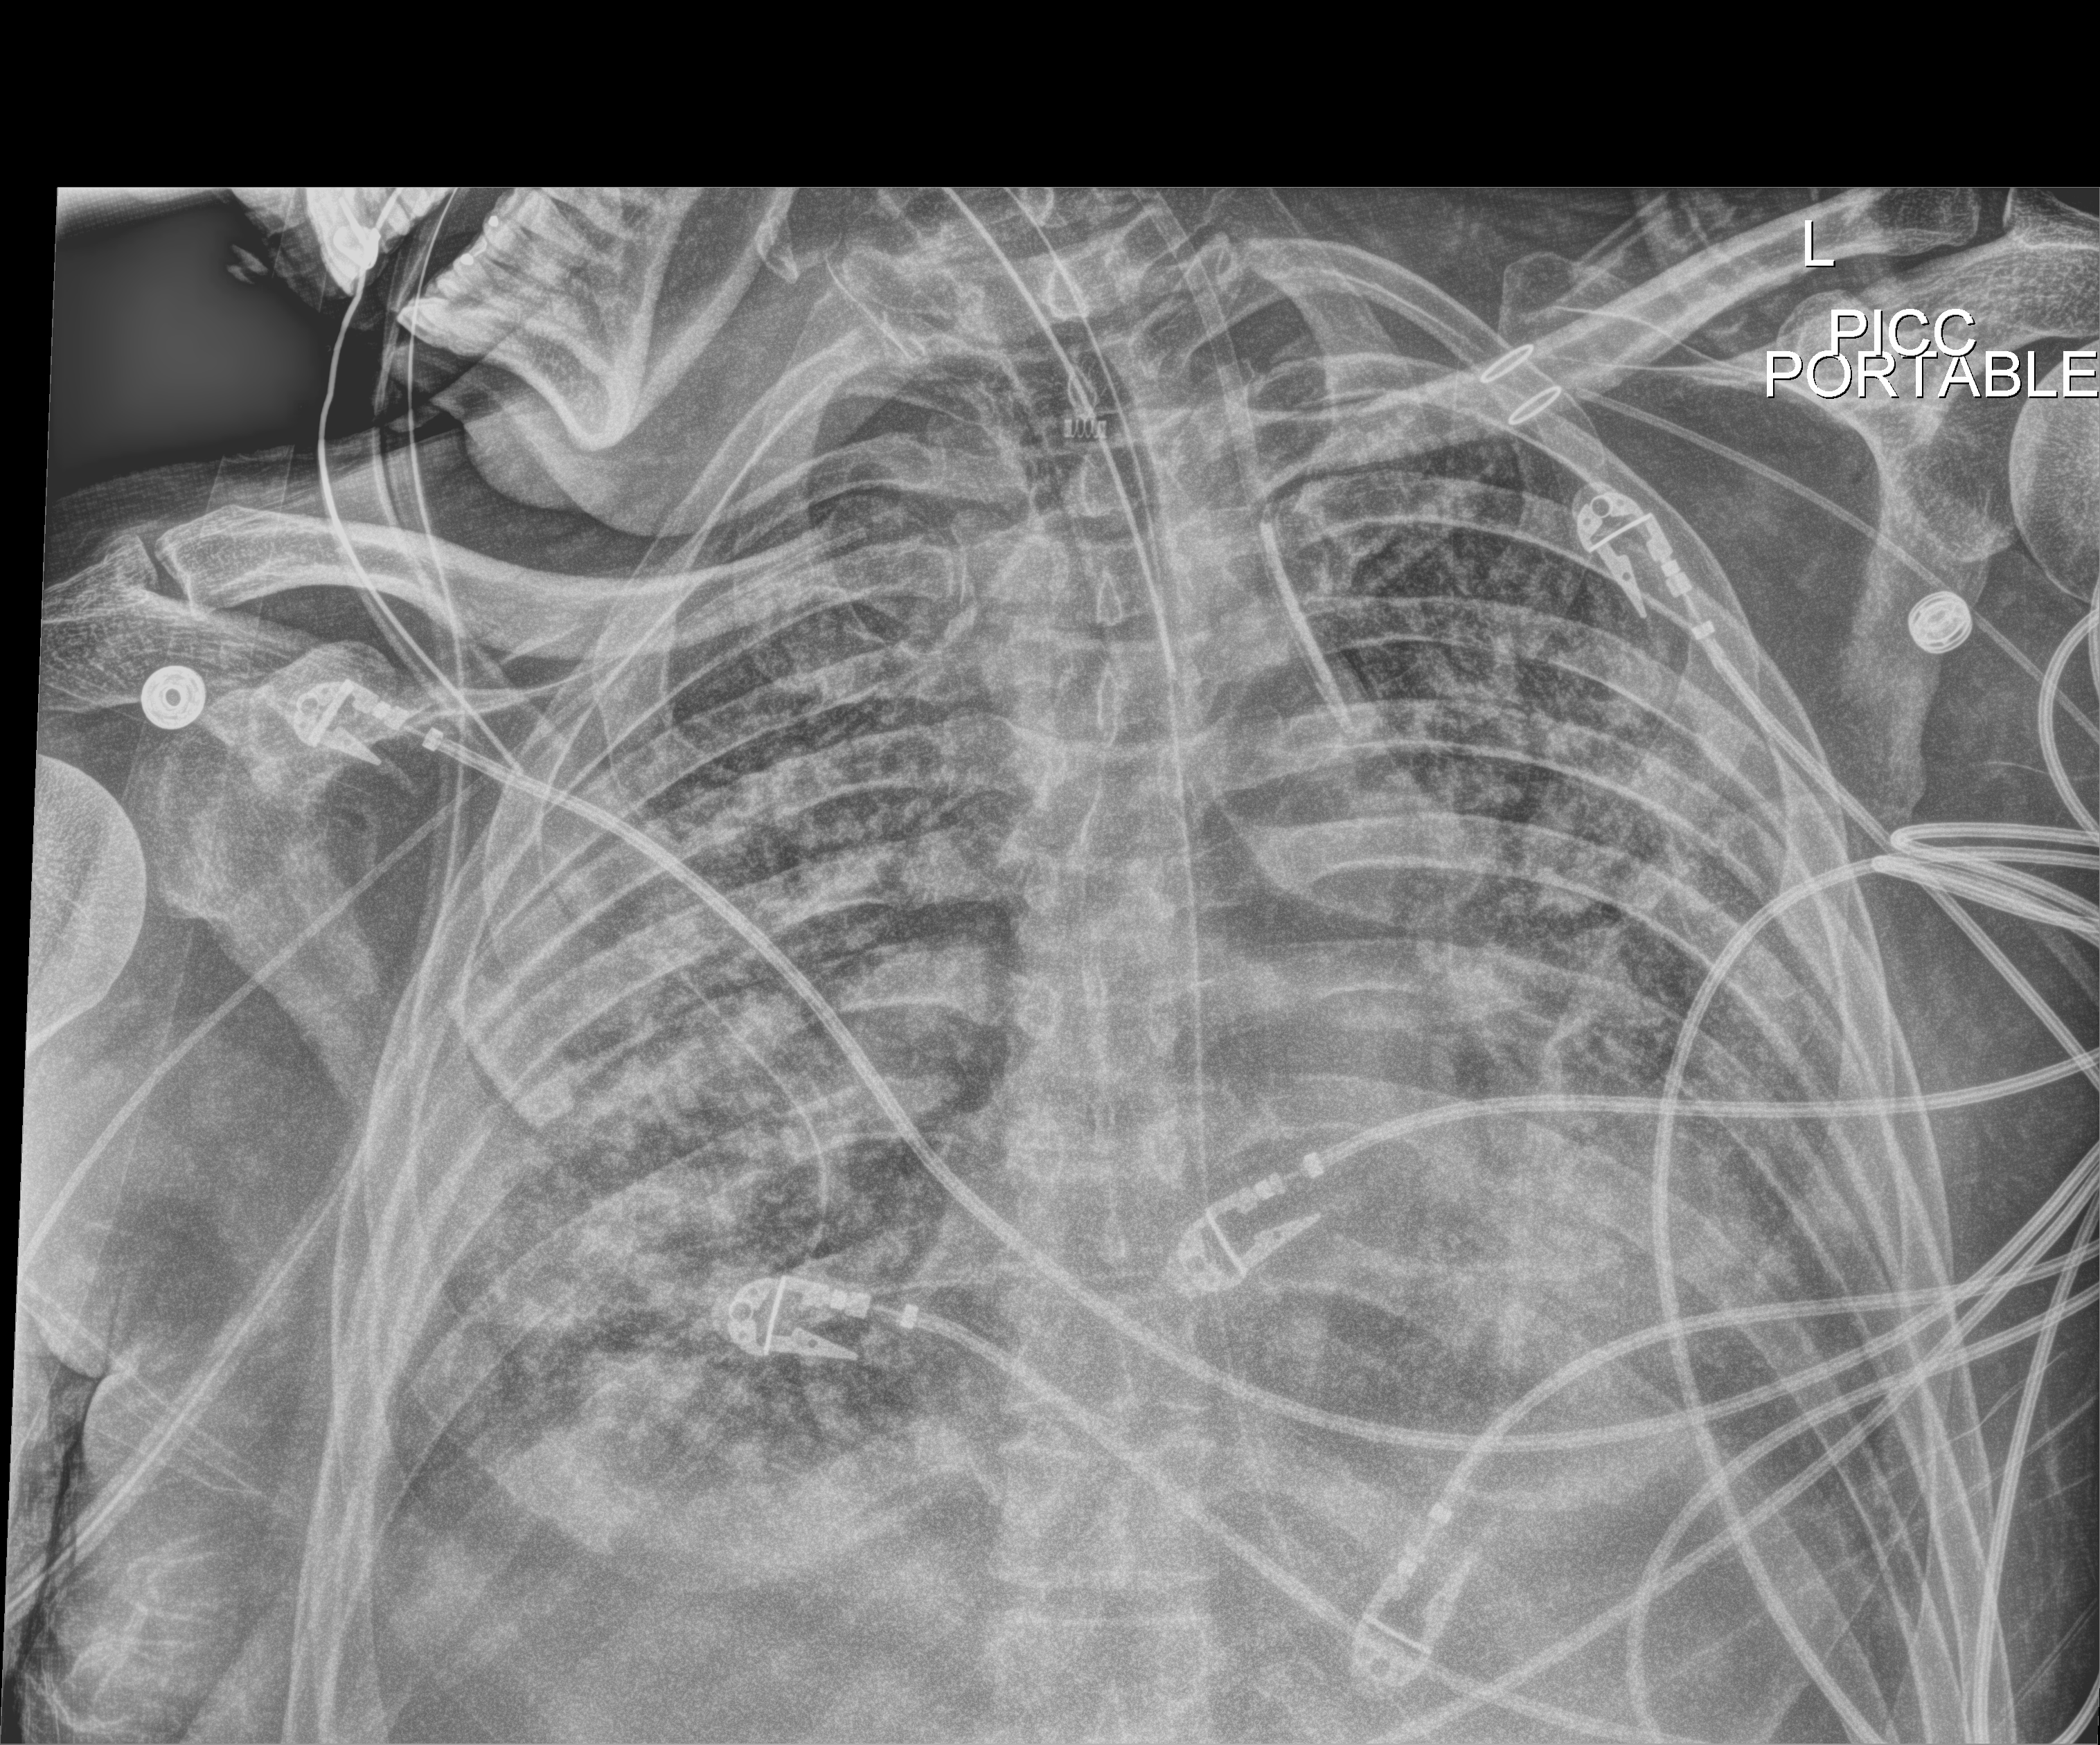
Portable chest radiograph. Patient hospitalised with COVID-19; male, aged 18–59 years.
From the hospital-stay record, not from the radiograph (when in the stay this image was taken is not recorded): admitted to intensive care during this hospital stay: yes.